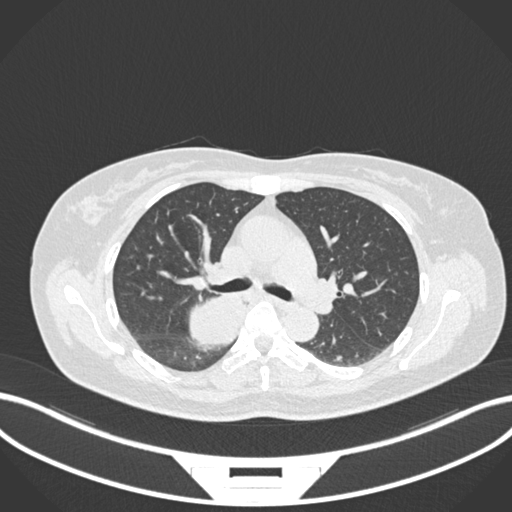
Chest CT, one axial slice; 120 kVp; lung window (W 1500 / L -600 HU); 1 mm slice thickness; 512 × 512 image matrix. Patient: female, 54 years. From the clinical record (not read from this slice): clinical TNM (as recorded): T4 N0 M0.
Annotated regions visible in this slice (rectangle marked by the reading radiologist):
- lung tumour (recorded histology: adenocarcinoma): bounding box <182,286,251,349> (left, top, right, bottom; pixels)